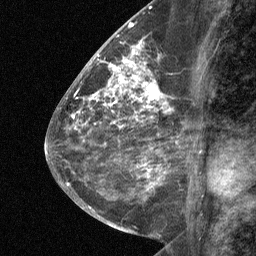
Breast MRI (dynamic contrast-enhanced), one sagittal slice. Position 29 of 64 along the scan axis. Dynamic contrast-enhanced study with each time point stored as its own series, time point 2 of 3 at this slice position (early post-contrast, ordered by acquisition time). 1.5 T. TE 4.8 ms, TR 27 ms. 256 × 256 image matrix. Female patient, age 59 years. From the clinical record (not read from this slice): setting: breast cancer imaged before/during neoadjuvant chemotherapy; receptor status: triple-negative.
Annotated regions visible in this slice (semi-automatic segmentation, software-assisted and operator-edited):
- analysis volume of interest (the breast-tissue region the enhancement analysis was run in; not a lesion): bounding box (x1, y1, x2, y2) in pixels: (122, 58, 166, 109)
- tumour enhancement mask (voxels above the 90 % enhancement threshold inside the analysis volume of interest): (122, 59, 158, 100)